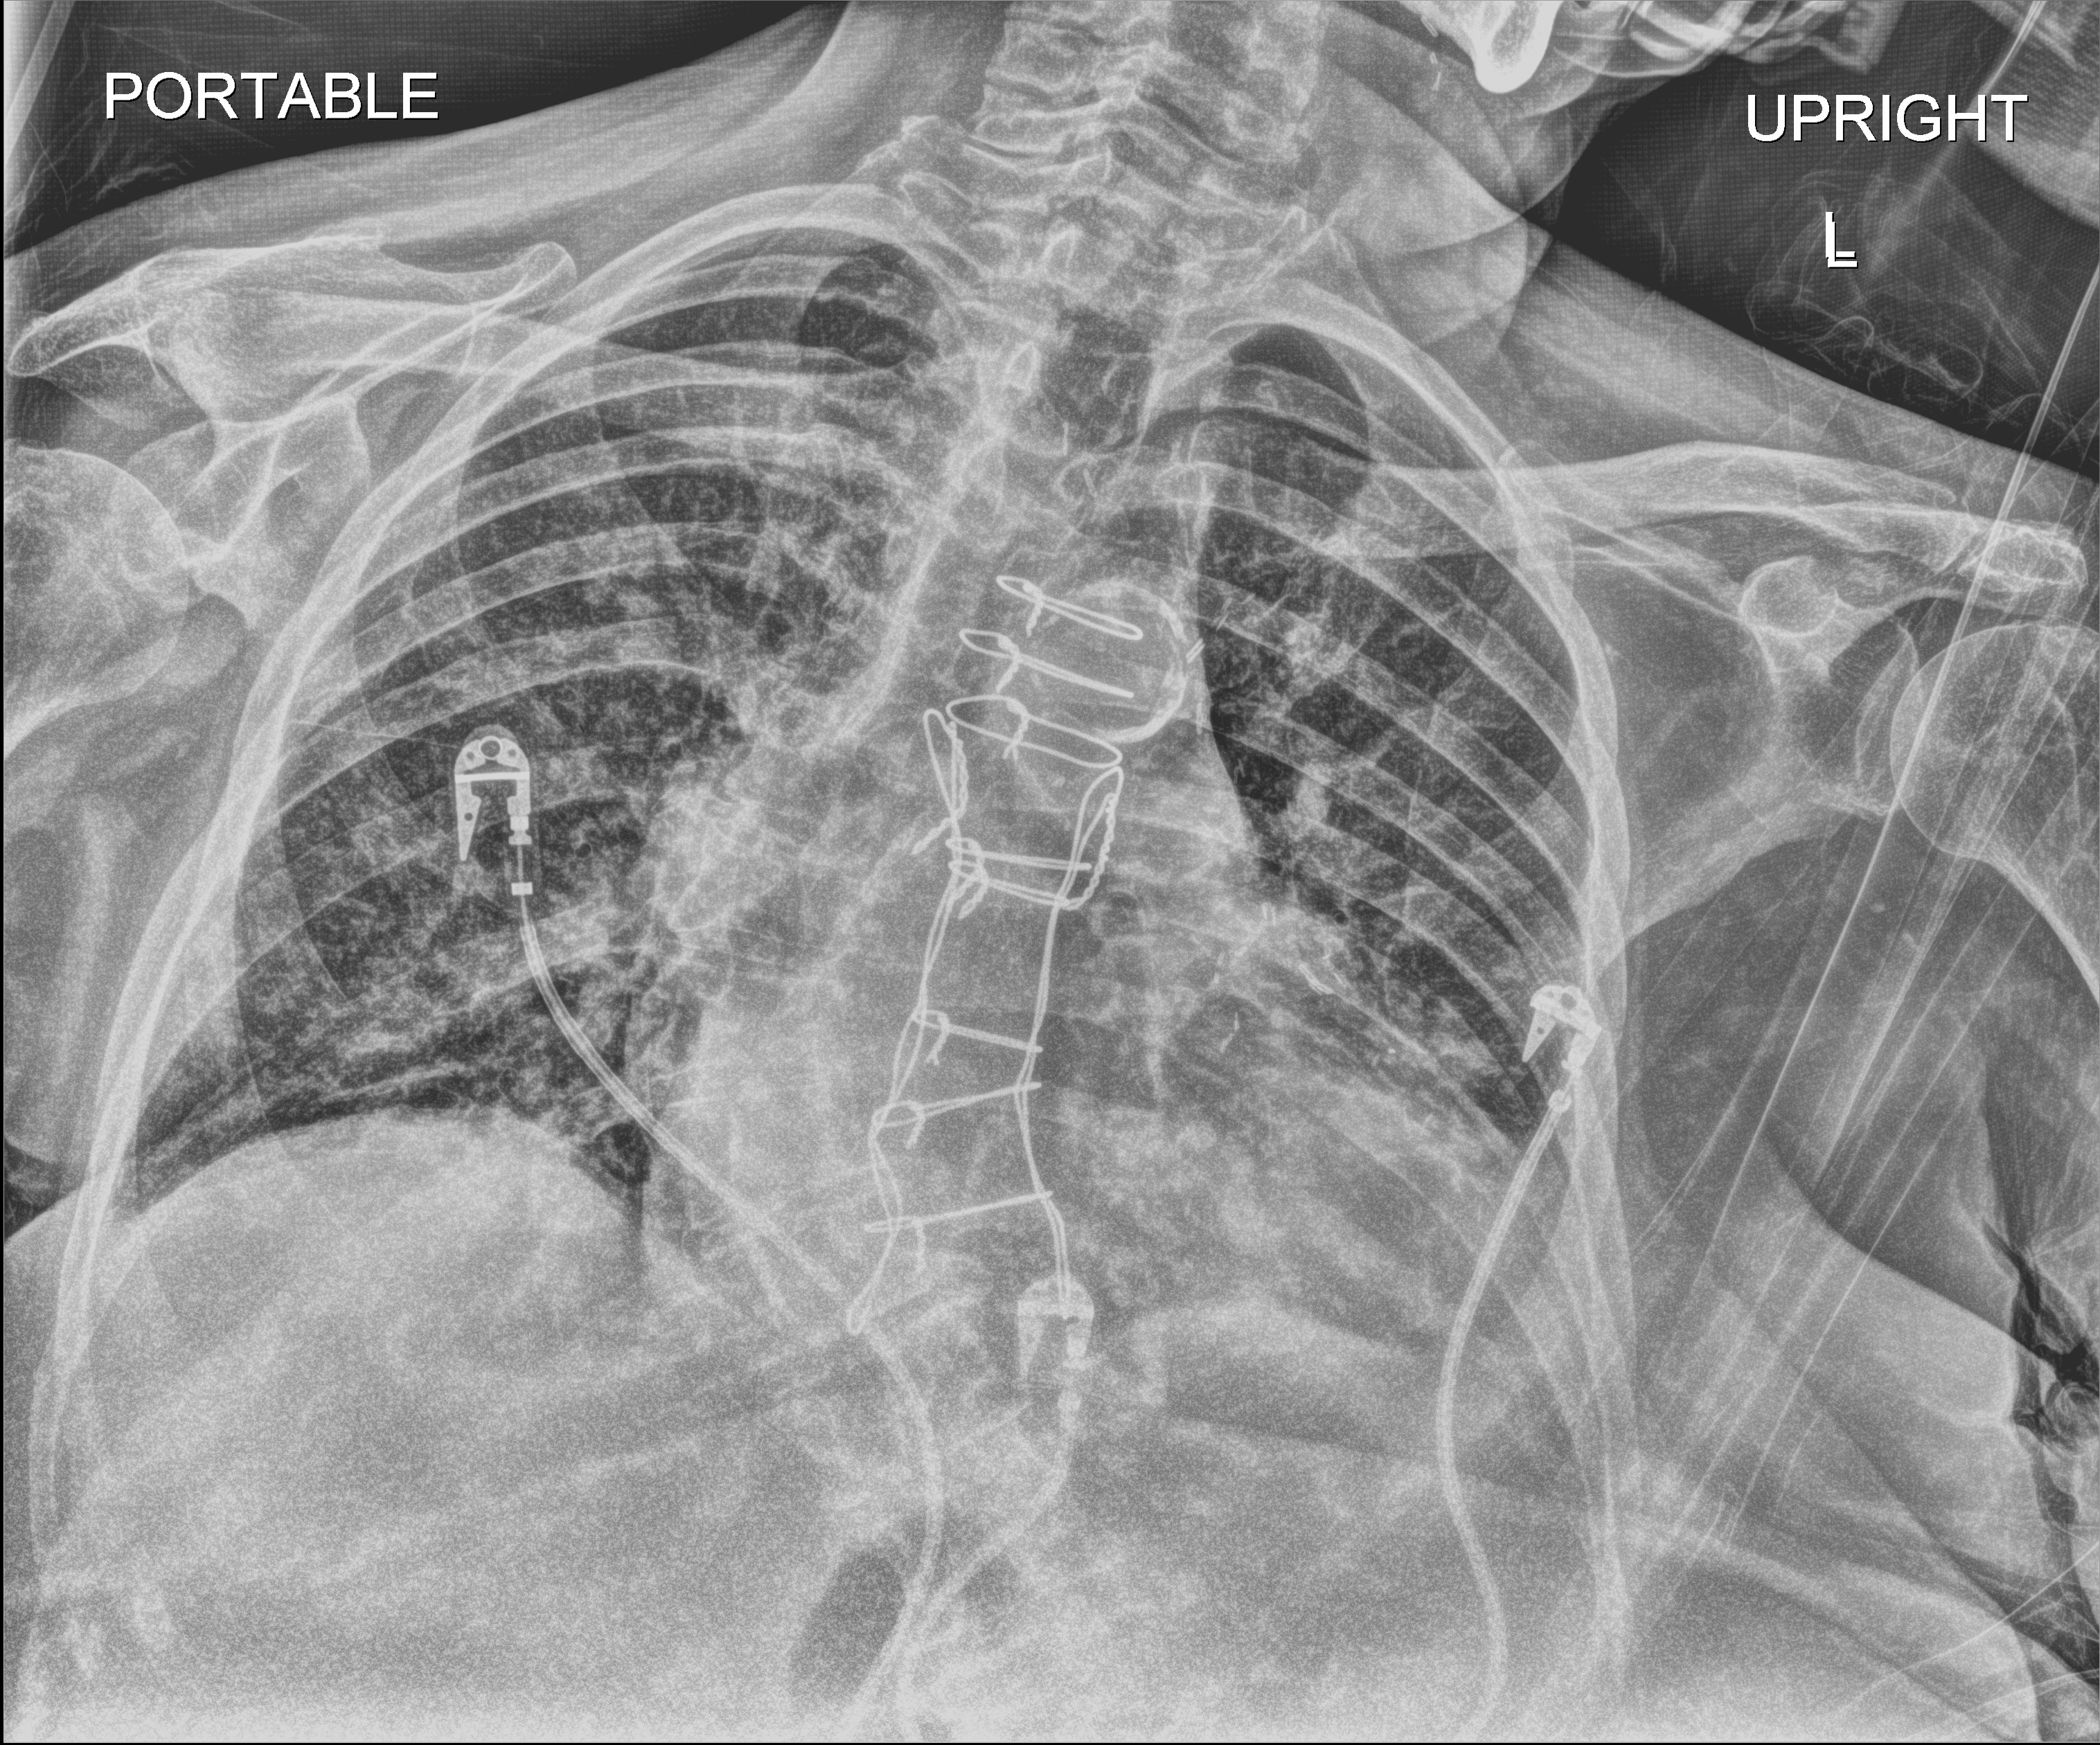
Portable chest radiograph; anteroposterior (AP) projection. Female patient hospitalised with COVID-19, age 75–90 years.
Hospital-stay facts (about this admission, not read from this image; timing relative to this image not recorded): admitted to intensive care during this hospital stay: no; mechanically ventilated during this hospital stay: no.